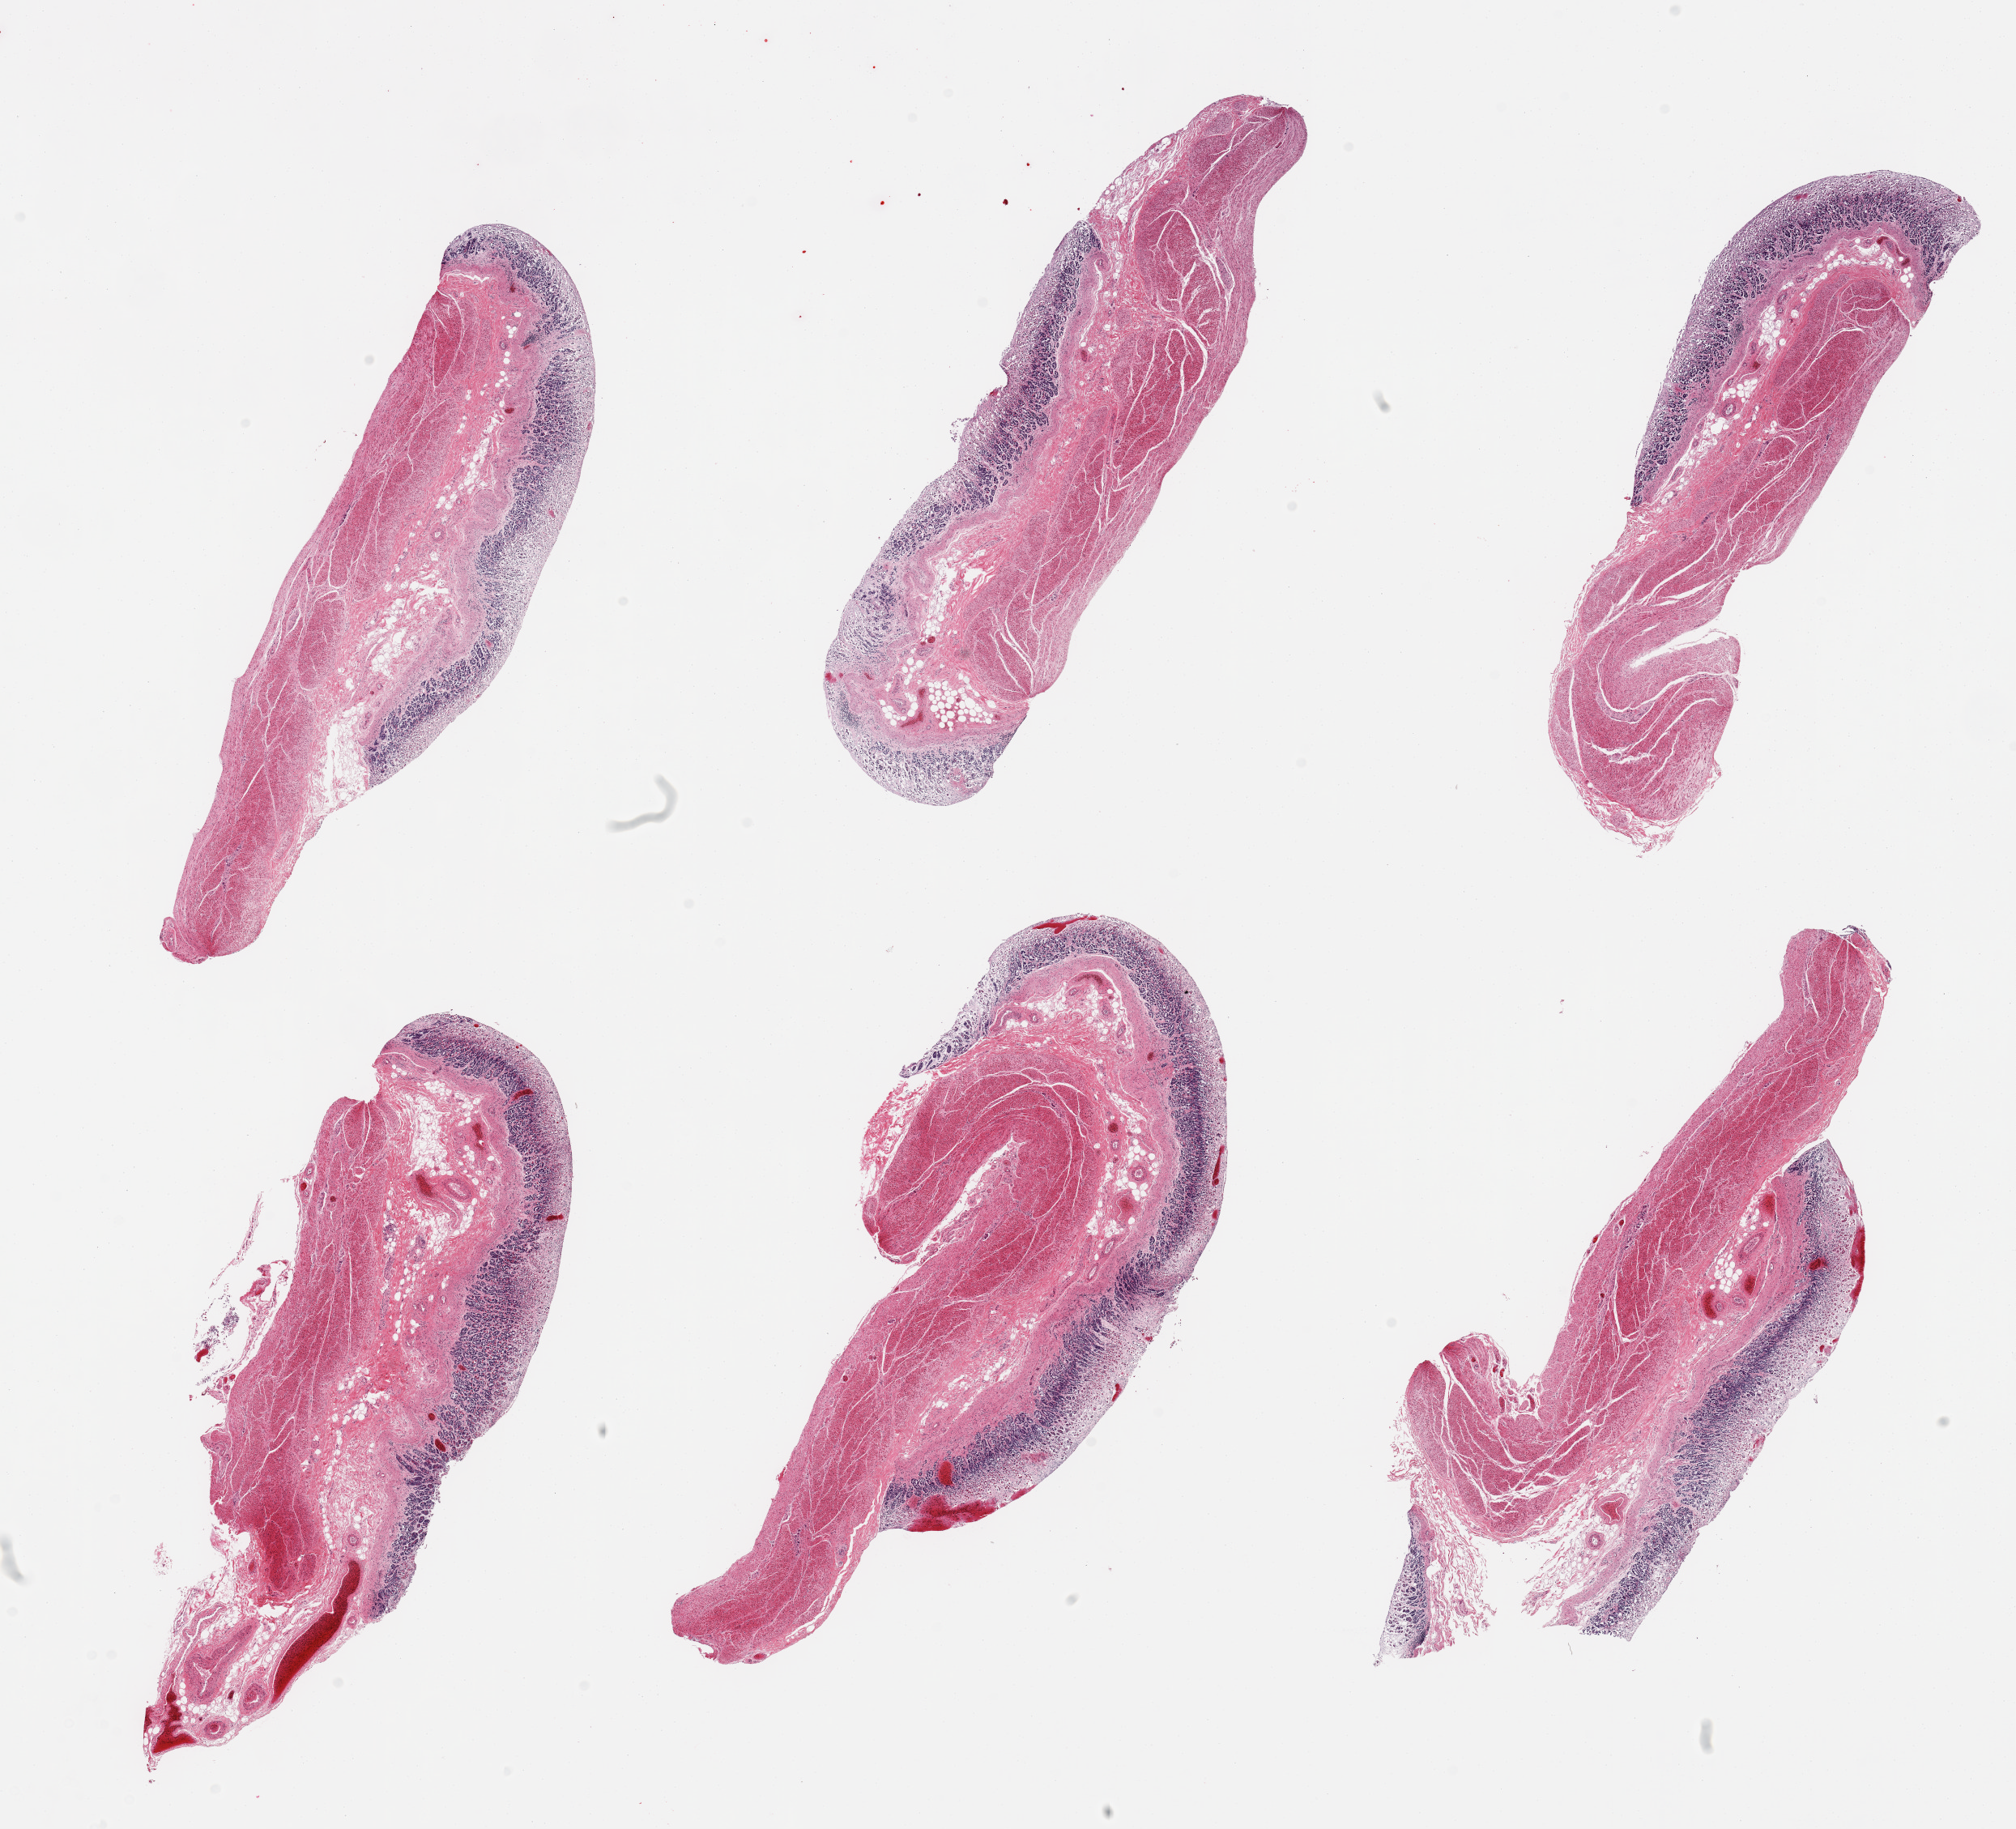
Digitized haematoxylin and eosin-stained section, brightfield — shown as a low-resolution overview of the whole scanned area (about 19.7 x 17.9 mm). PAXgene-fixed paraffin-embedded (PFPE) section. Target tissue: stomach. Tissue donor sample.
Pathologist's review note for this sample: 6 pieces, mucosa up to ~0.6mm, near- total autolysis.